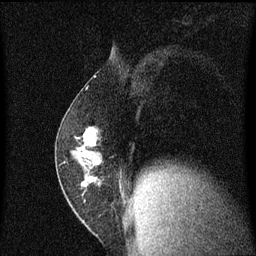
Breast MRI (dynamic contrast-enhanced), one sagittal slice. Slice 32 of 60 in the series (ordered by position). Dynamic contrast-enhanced series, image 2 of 3 at this slice position (ordered by acquisition). 1.5 T. TE 4.2 ms, TR 8.4 ms. 2 mm slice thickness. 256 × 256 image matrix, field of view 200 × 200 mm. Patient: female, 52 years. Case-level facts recorded for this patient, not image findings: setting: breast cancer imaged before/during neoadjuvant chemotherapy; receptor status: HER2-positive.
Outlined on this slice (semi-automatic segmentation, software-assisted and operator-edited):
- analysis volume of interest (the breast-tissue region the enhancement analysis was run in; not a lesion): bounding box [x1, y1, x2, y2] px = [56, 124, 106, 191]
- tumour enhancement mask (voxels above the 70 % enhancement threshold inside the analysis volume of interest): [72, 128, 97, 187]